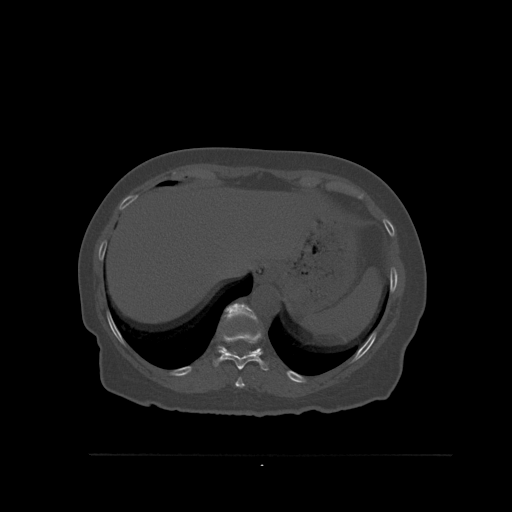
CT including the spine, one axial slice. Slice 317 of 527 in the series (ordered by position). Bone window (W 1800 / L 400 HU). 1.5 mm slice thickness. 512 × 512 image matrix. Patient: female, 73 years. From the clinical record (not read from this slice): primary cancer: breast.
Annotated regions visible in this slice (semi-automatic segmentation, software-assisted and operator-edited):
- T10 vertebra: box from (x=213, y=332) to (x=269, y=371) px
- T11 vertebra: (x=217, y=303)–(x=262, y=356)
- T9 vertebra: (x=235, y=377)–(x=245, y=388)